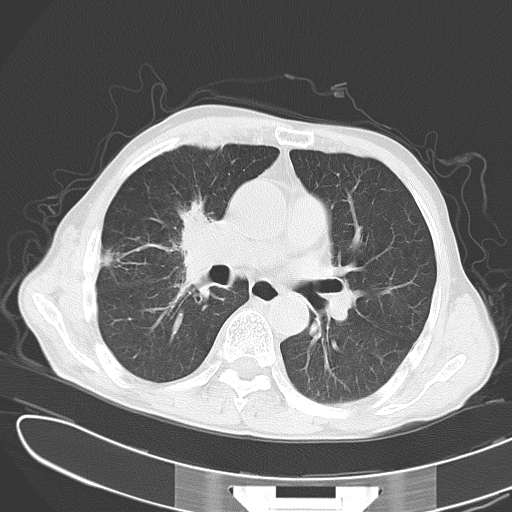
Chest CT, one axial slice; slice 19 of 43 in the series (ordered by position); reconstruction kernel B70f; 120 kVp; lung window (W 1500 / L -600 HU); 5 mm slice thickness; 512 × 512 image matrix. Male patient, age 65 years. Case-level facts recorded for this patient, not image findings: clinical TNM (as recorded): T2 N3 M1; histopathological grade: G3.
Annotated regions visible in this slice (rectangle marked by the reading radiologist):
- lung tumour (recorded histology: small cell carcinoma): bounding box [x1, y1, x2, y2] px = [174, 195, 230, 291]